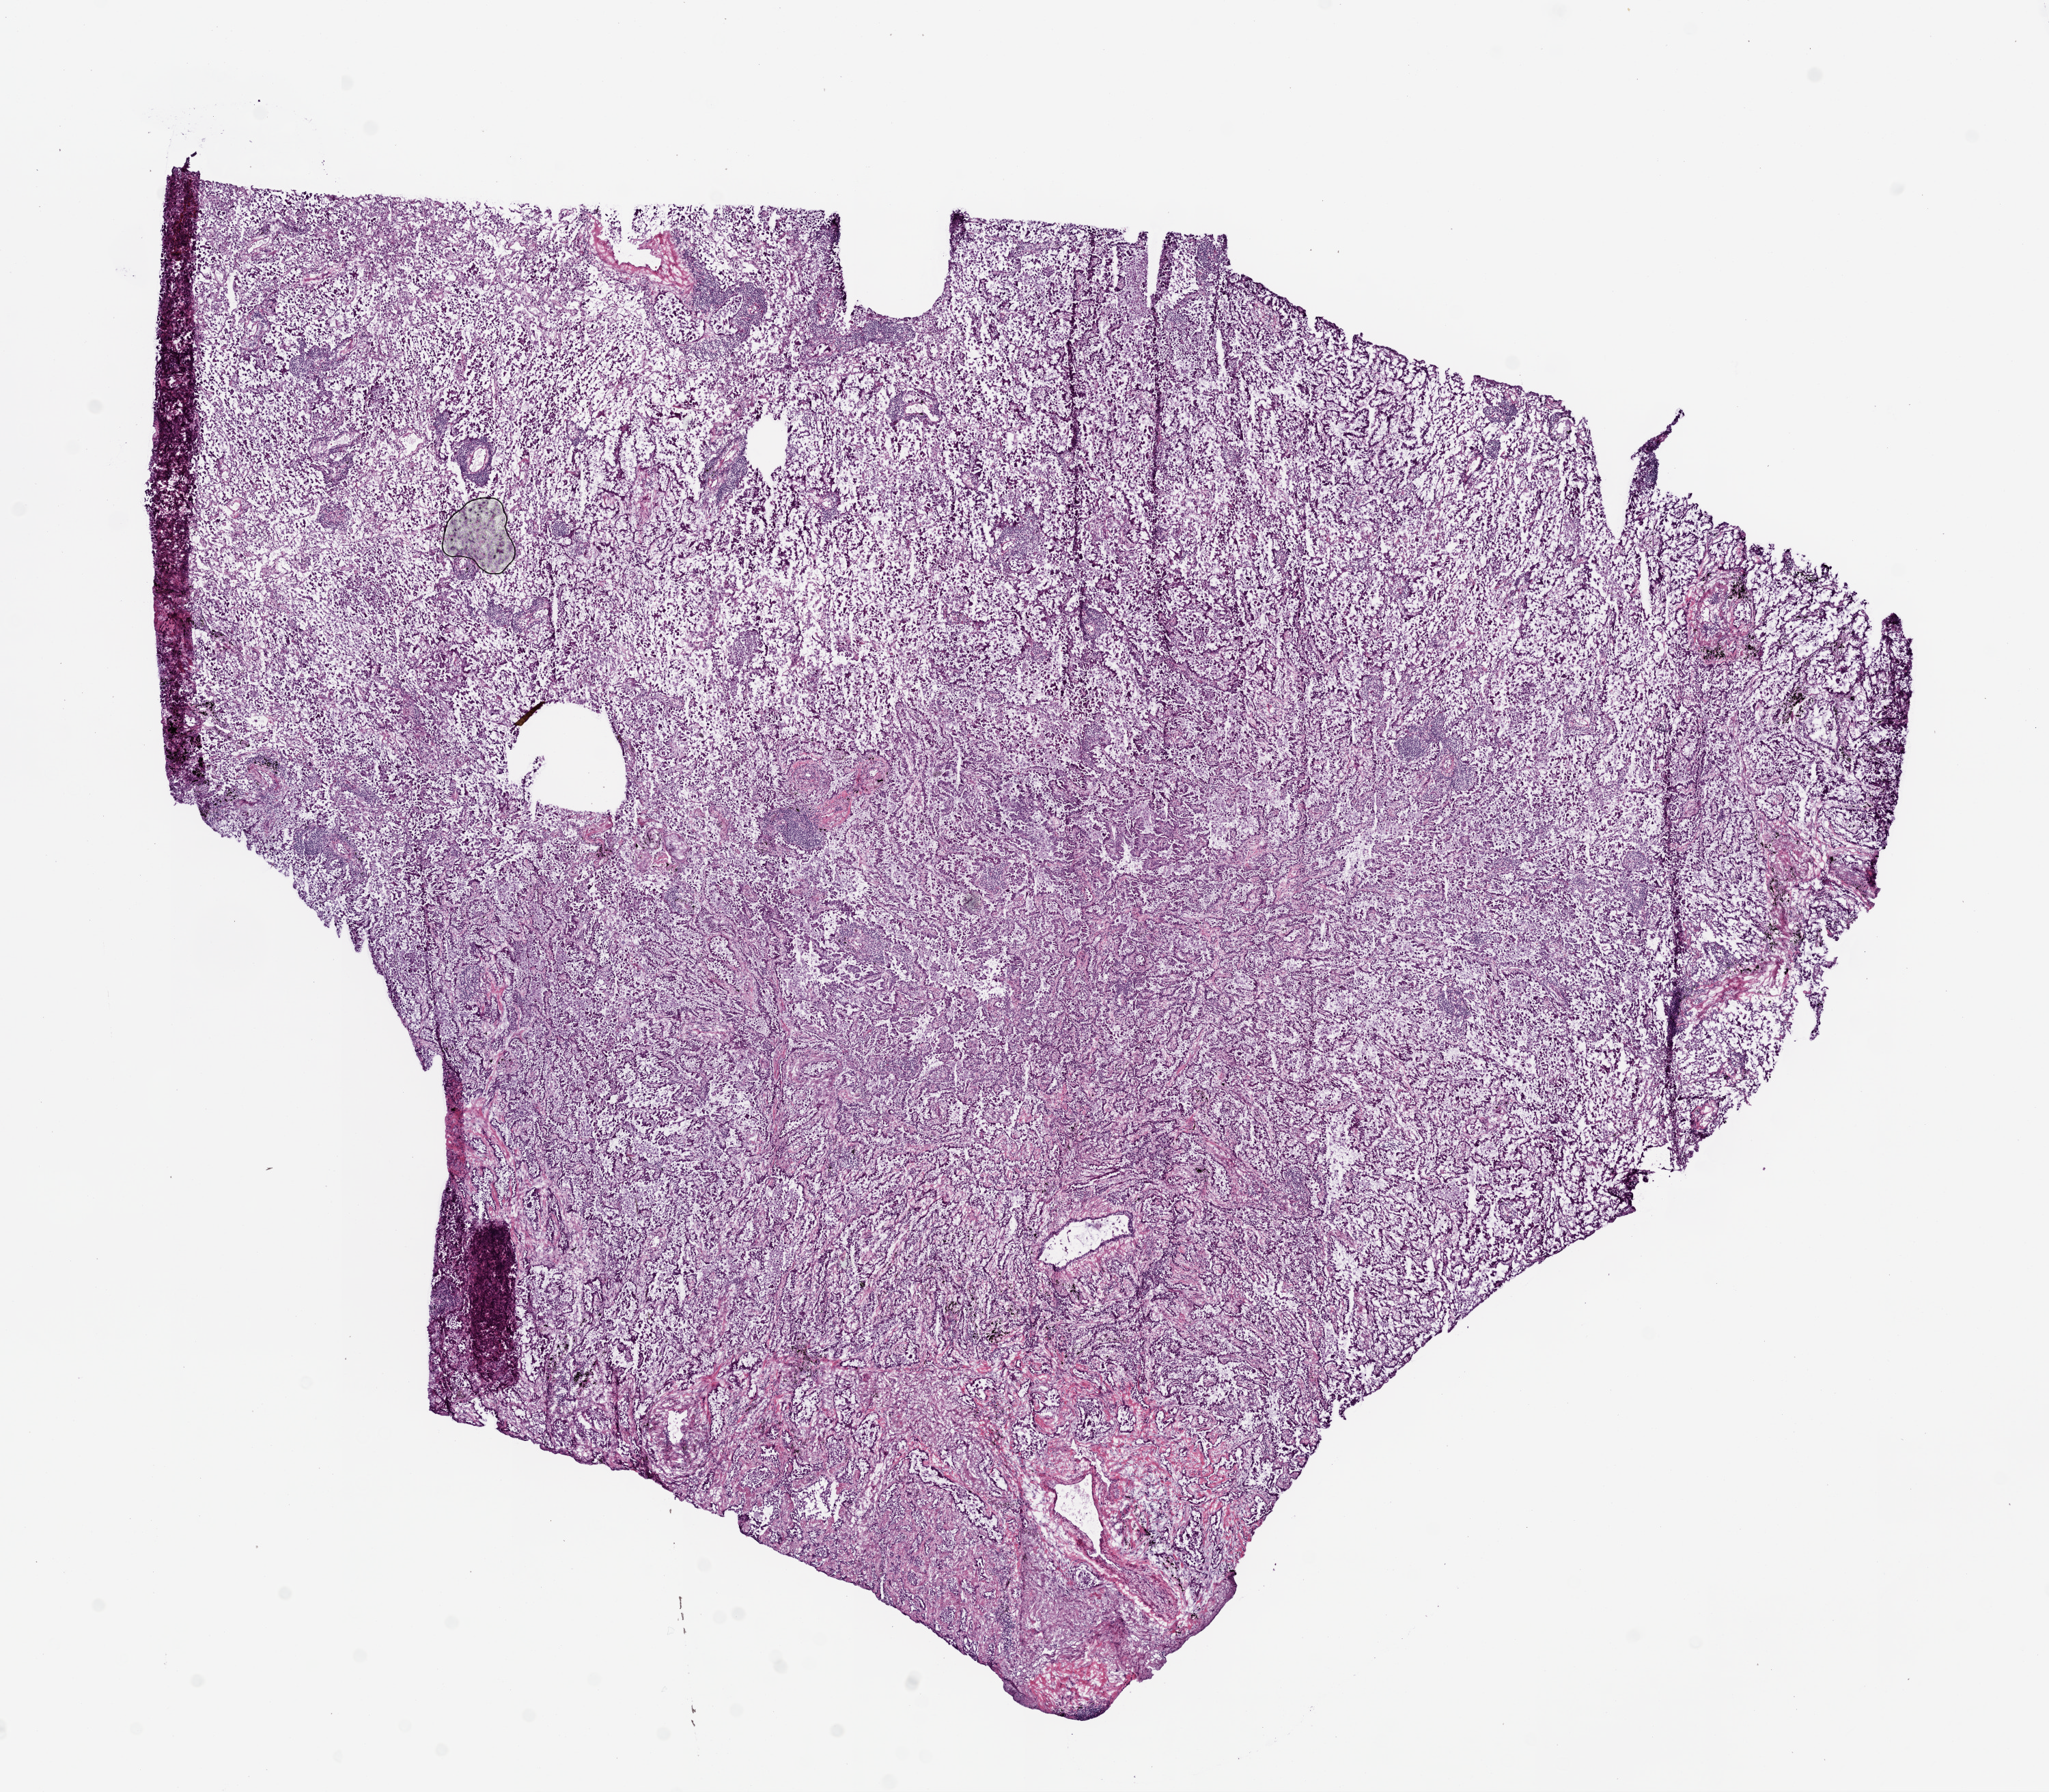
Digitized H&E-stained tissue section (whole slide) — whole scanned area (about 12.0 x 10.5 mm, acquisition: 20x scan) shown as a low-resolution overview. Frozen section from the bottom of the tissue portion. Lung, primary tumour sample. Male patient; age at initial diagnosis 65 years. Composition of this section per pathologist review: tumour cells 100%, tumour nuclei 80%, normal cells 0%, stromal cells 0%, necrosis 0%. Infiltration values recorded for this section: lymphocyte infiltration 15%, monocyte infiltration 4%, neutrophil infiltration 0%.
Laterality: left. Pathologic diagnosis: Adenocarcinoma with mixed subtypes. AJCC pathologic stage: IIB (6th edition).